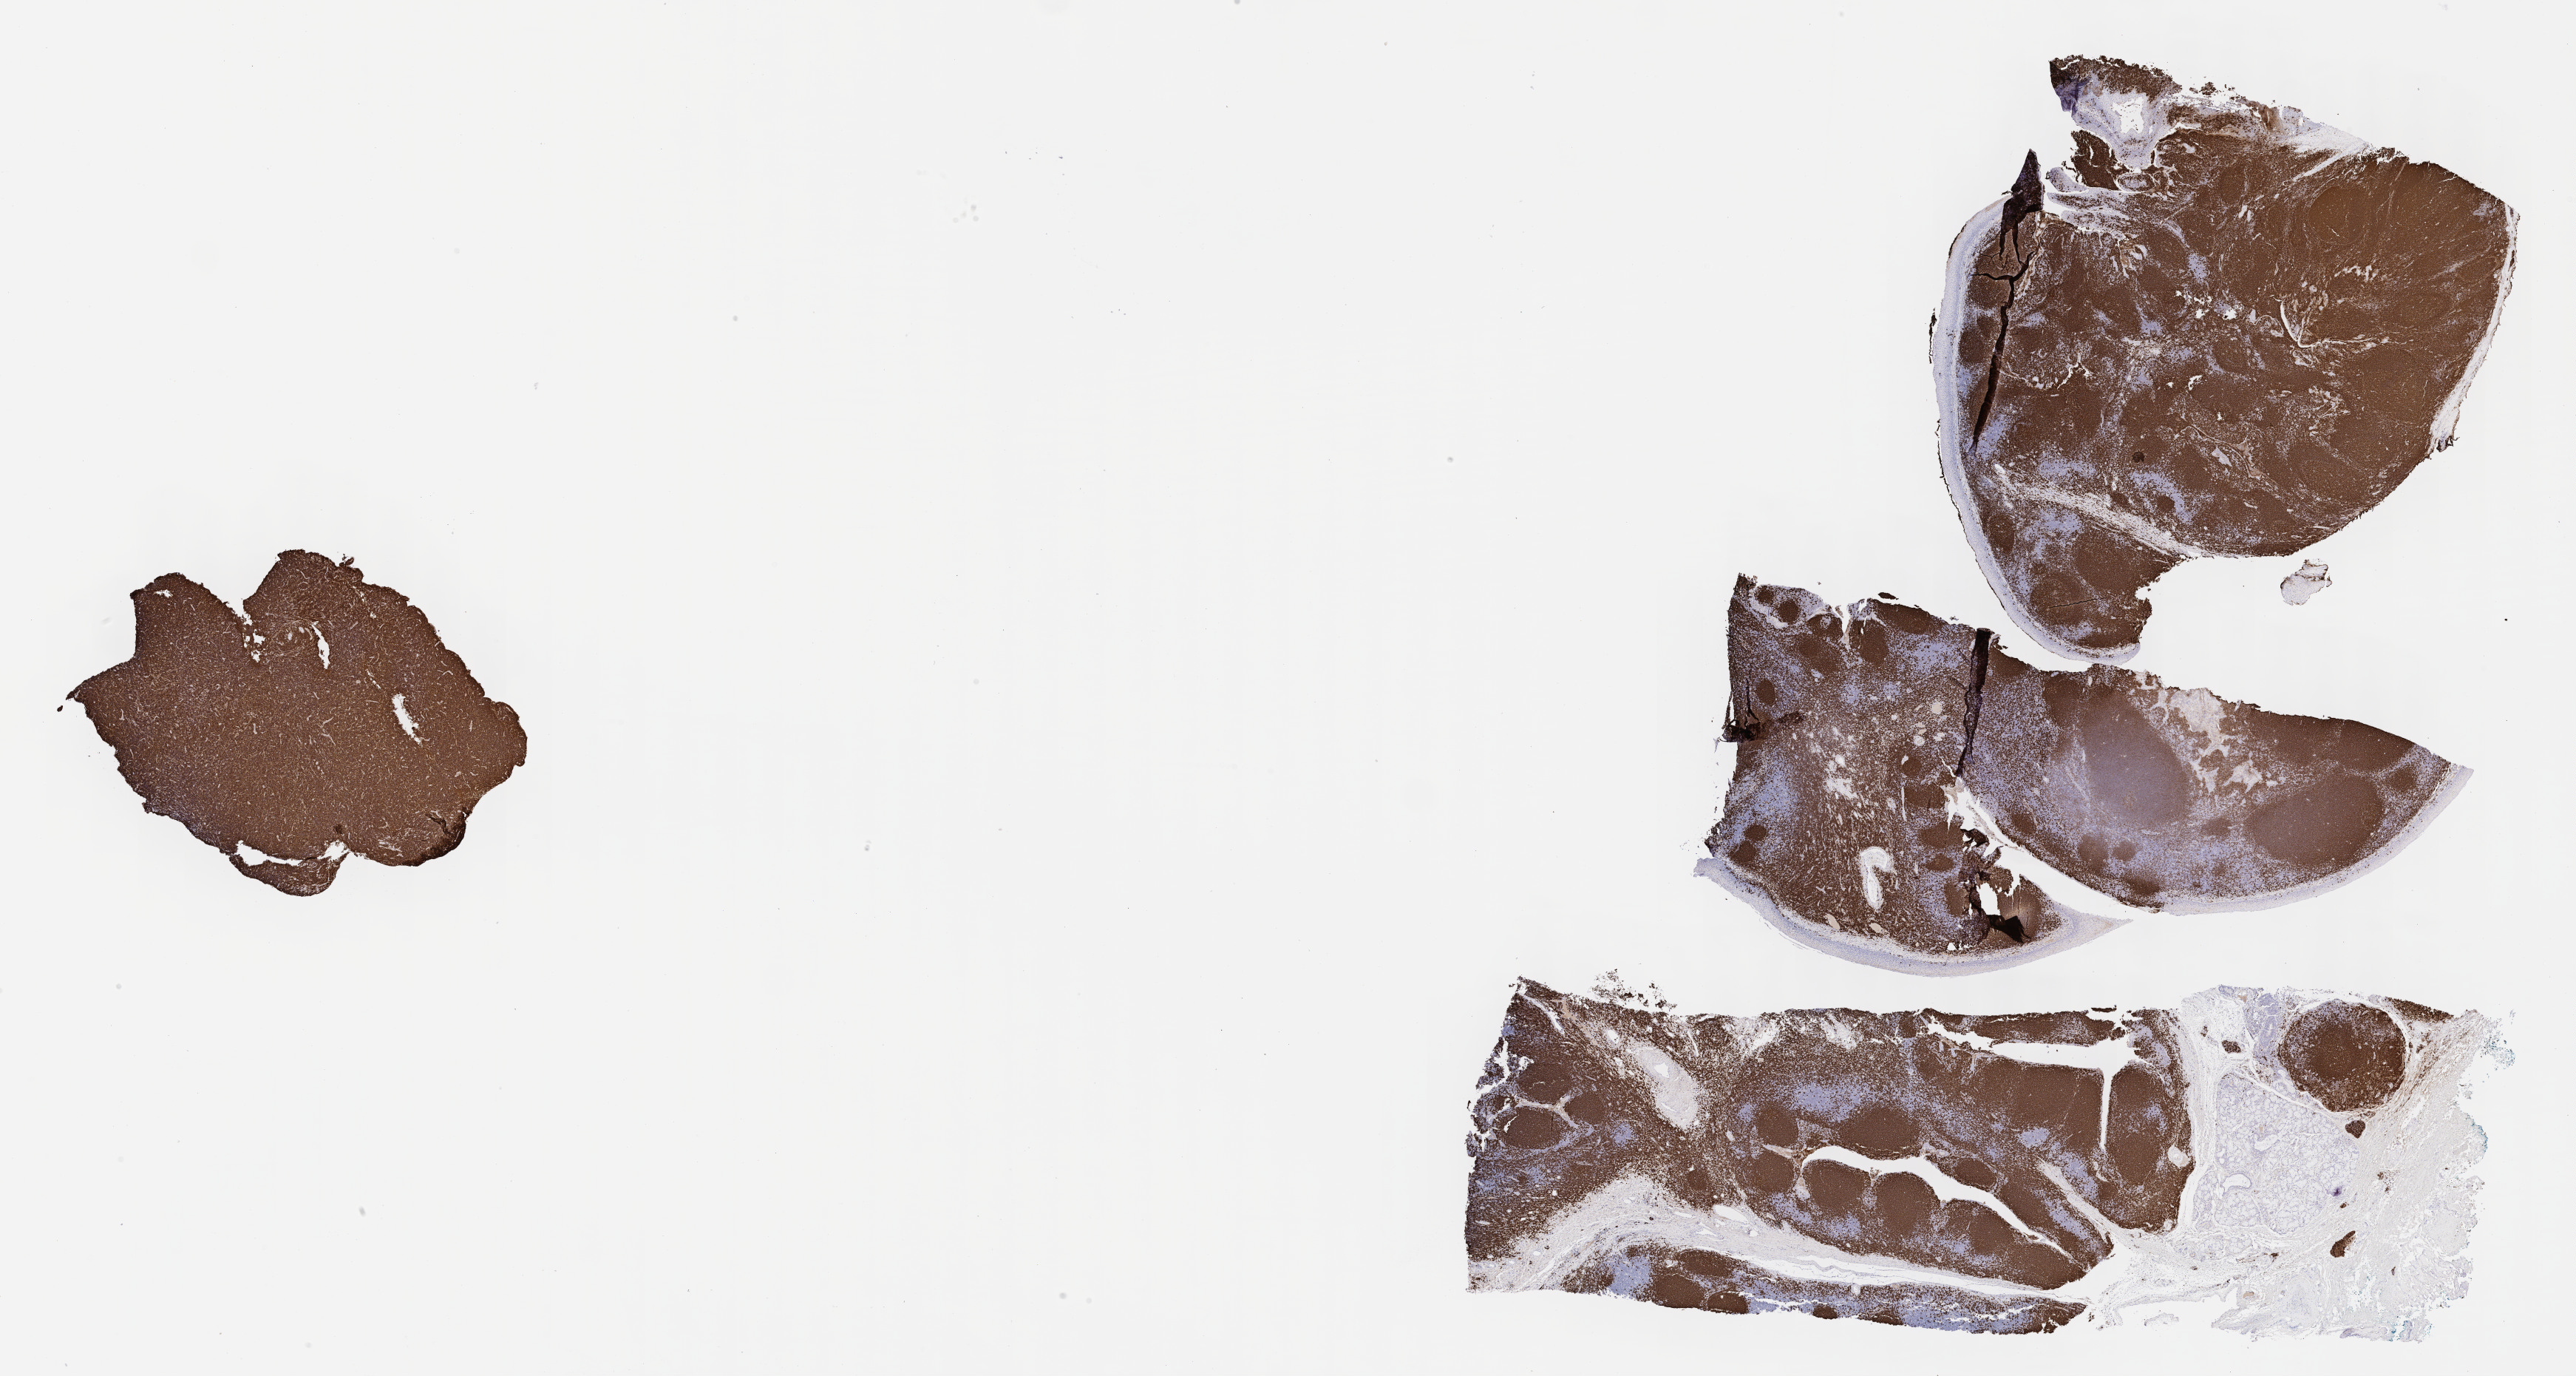
IHC for CD20, whole-slide image — low-resolution overview of the scanned area, about 28.2 x 15.0 mm; tumor tissue; site: mandible. Patient: male, age at initial diagnosis 8 years.
Histologic diagnosis: Burkitt lymphoma, NOS.